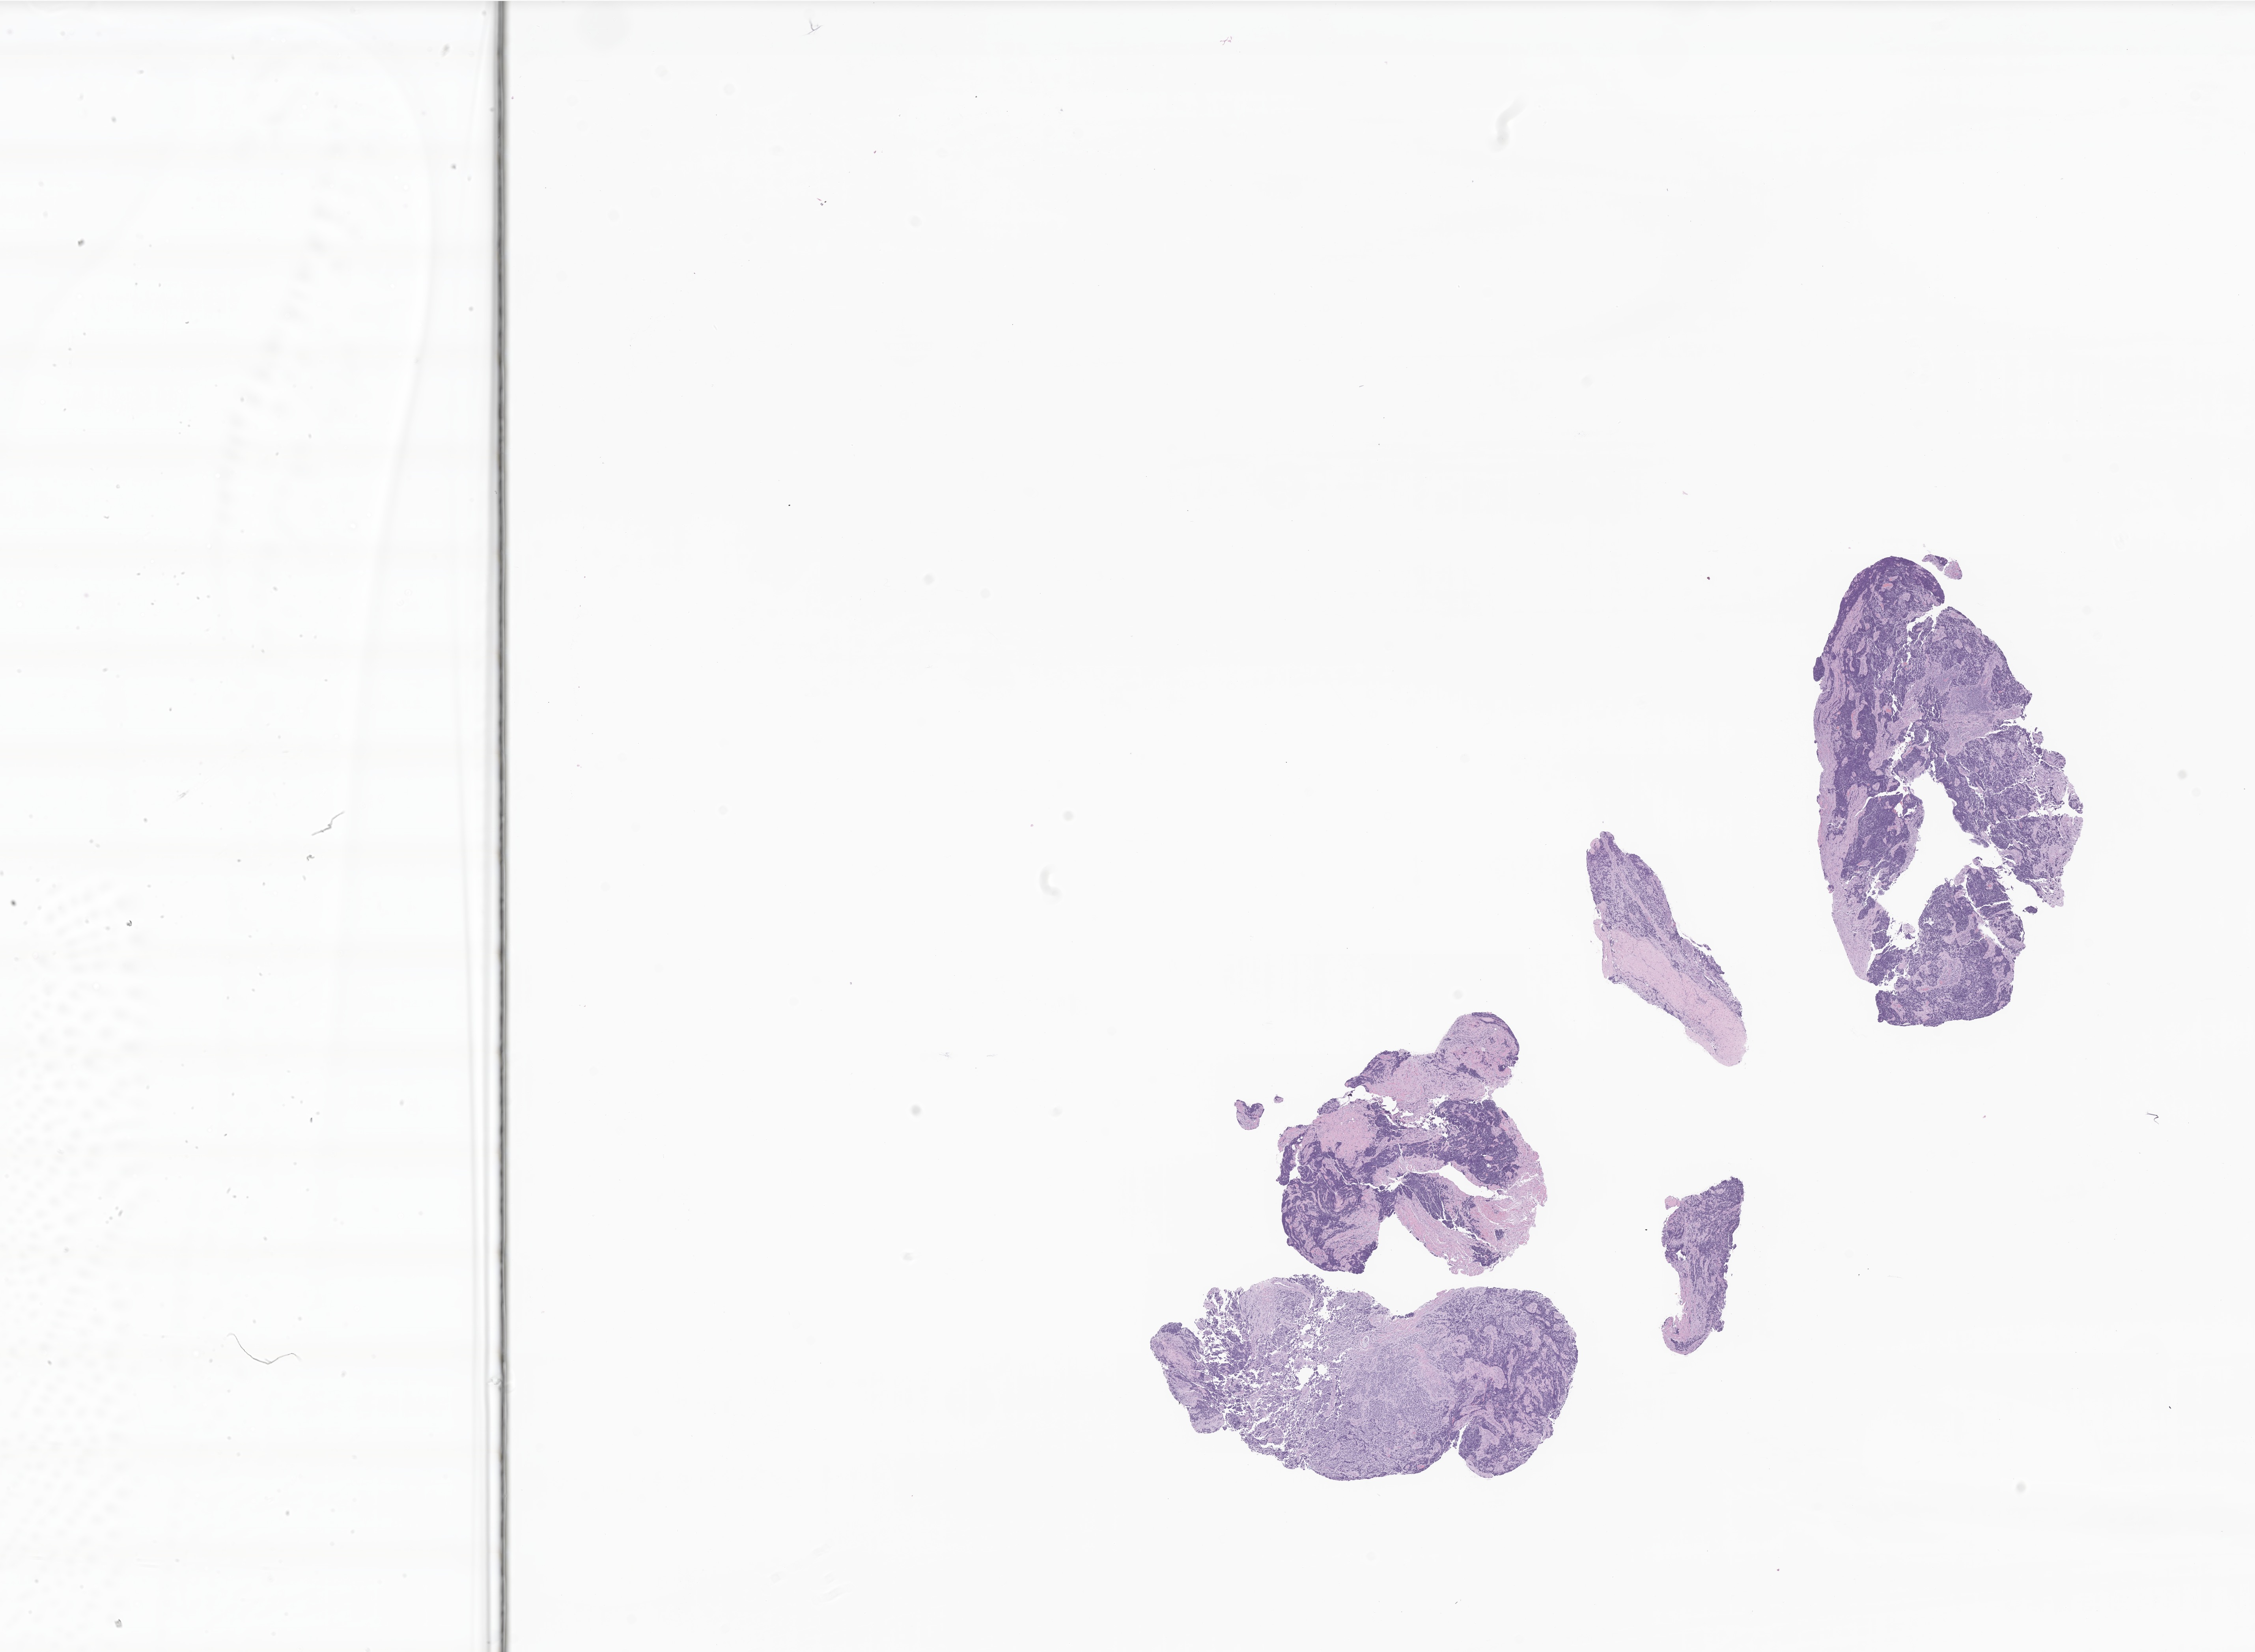
Whole-slide image, H&E stain of tumor tissue from the spinal cord, a low-resolution overview of the entire scanned area, about 24.1 x 17.7 mm; FFPE section. Male patient, age 440 days (about 1.2 years).
Recorded diagnosis: Neuroblastoma, NOS.